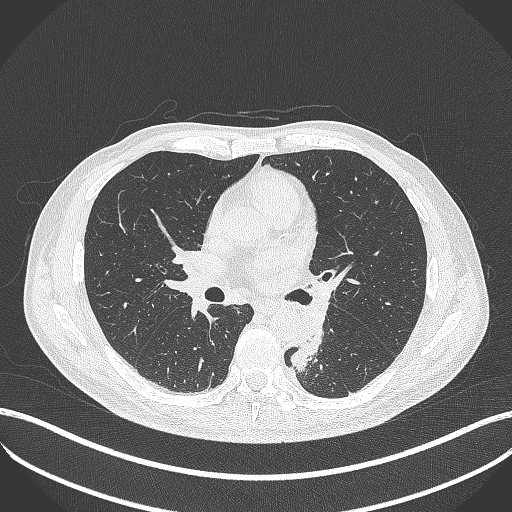
Chest CT, one axial slice; slice 222 of 451 in the series (ordered by position); reconstruction kernel B70f; 120 kVp; lung window (W 1500 / L -600 HU); 1 mm slice thickness; 512 × 512 image matrix, field of view 400 × 400 mm. Male patient, age 72 years. Case-level facts recorded for this patient, not image findings: clinical TNM (as recorded): T2b N0 M1.
Annotated regions visible in this slice (rectangle marked by the reading radiologist):
- lung tumour (recorded histology: adenocarcinoma): box from (x=286, y=328) to (x=326, y=375) px